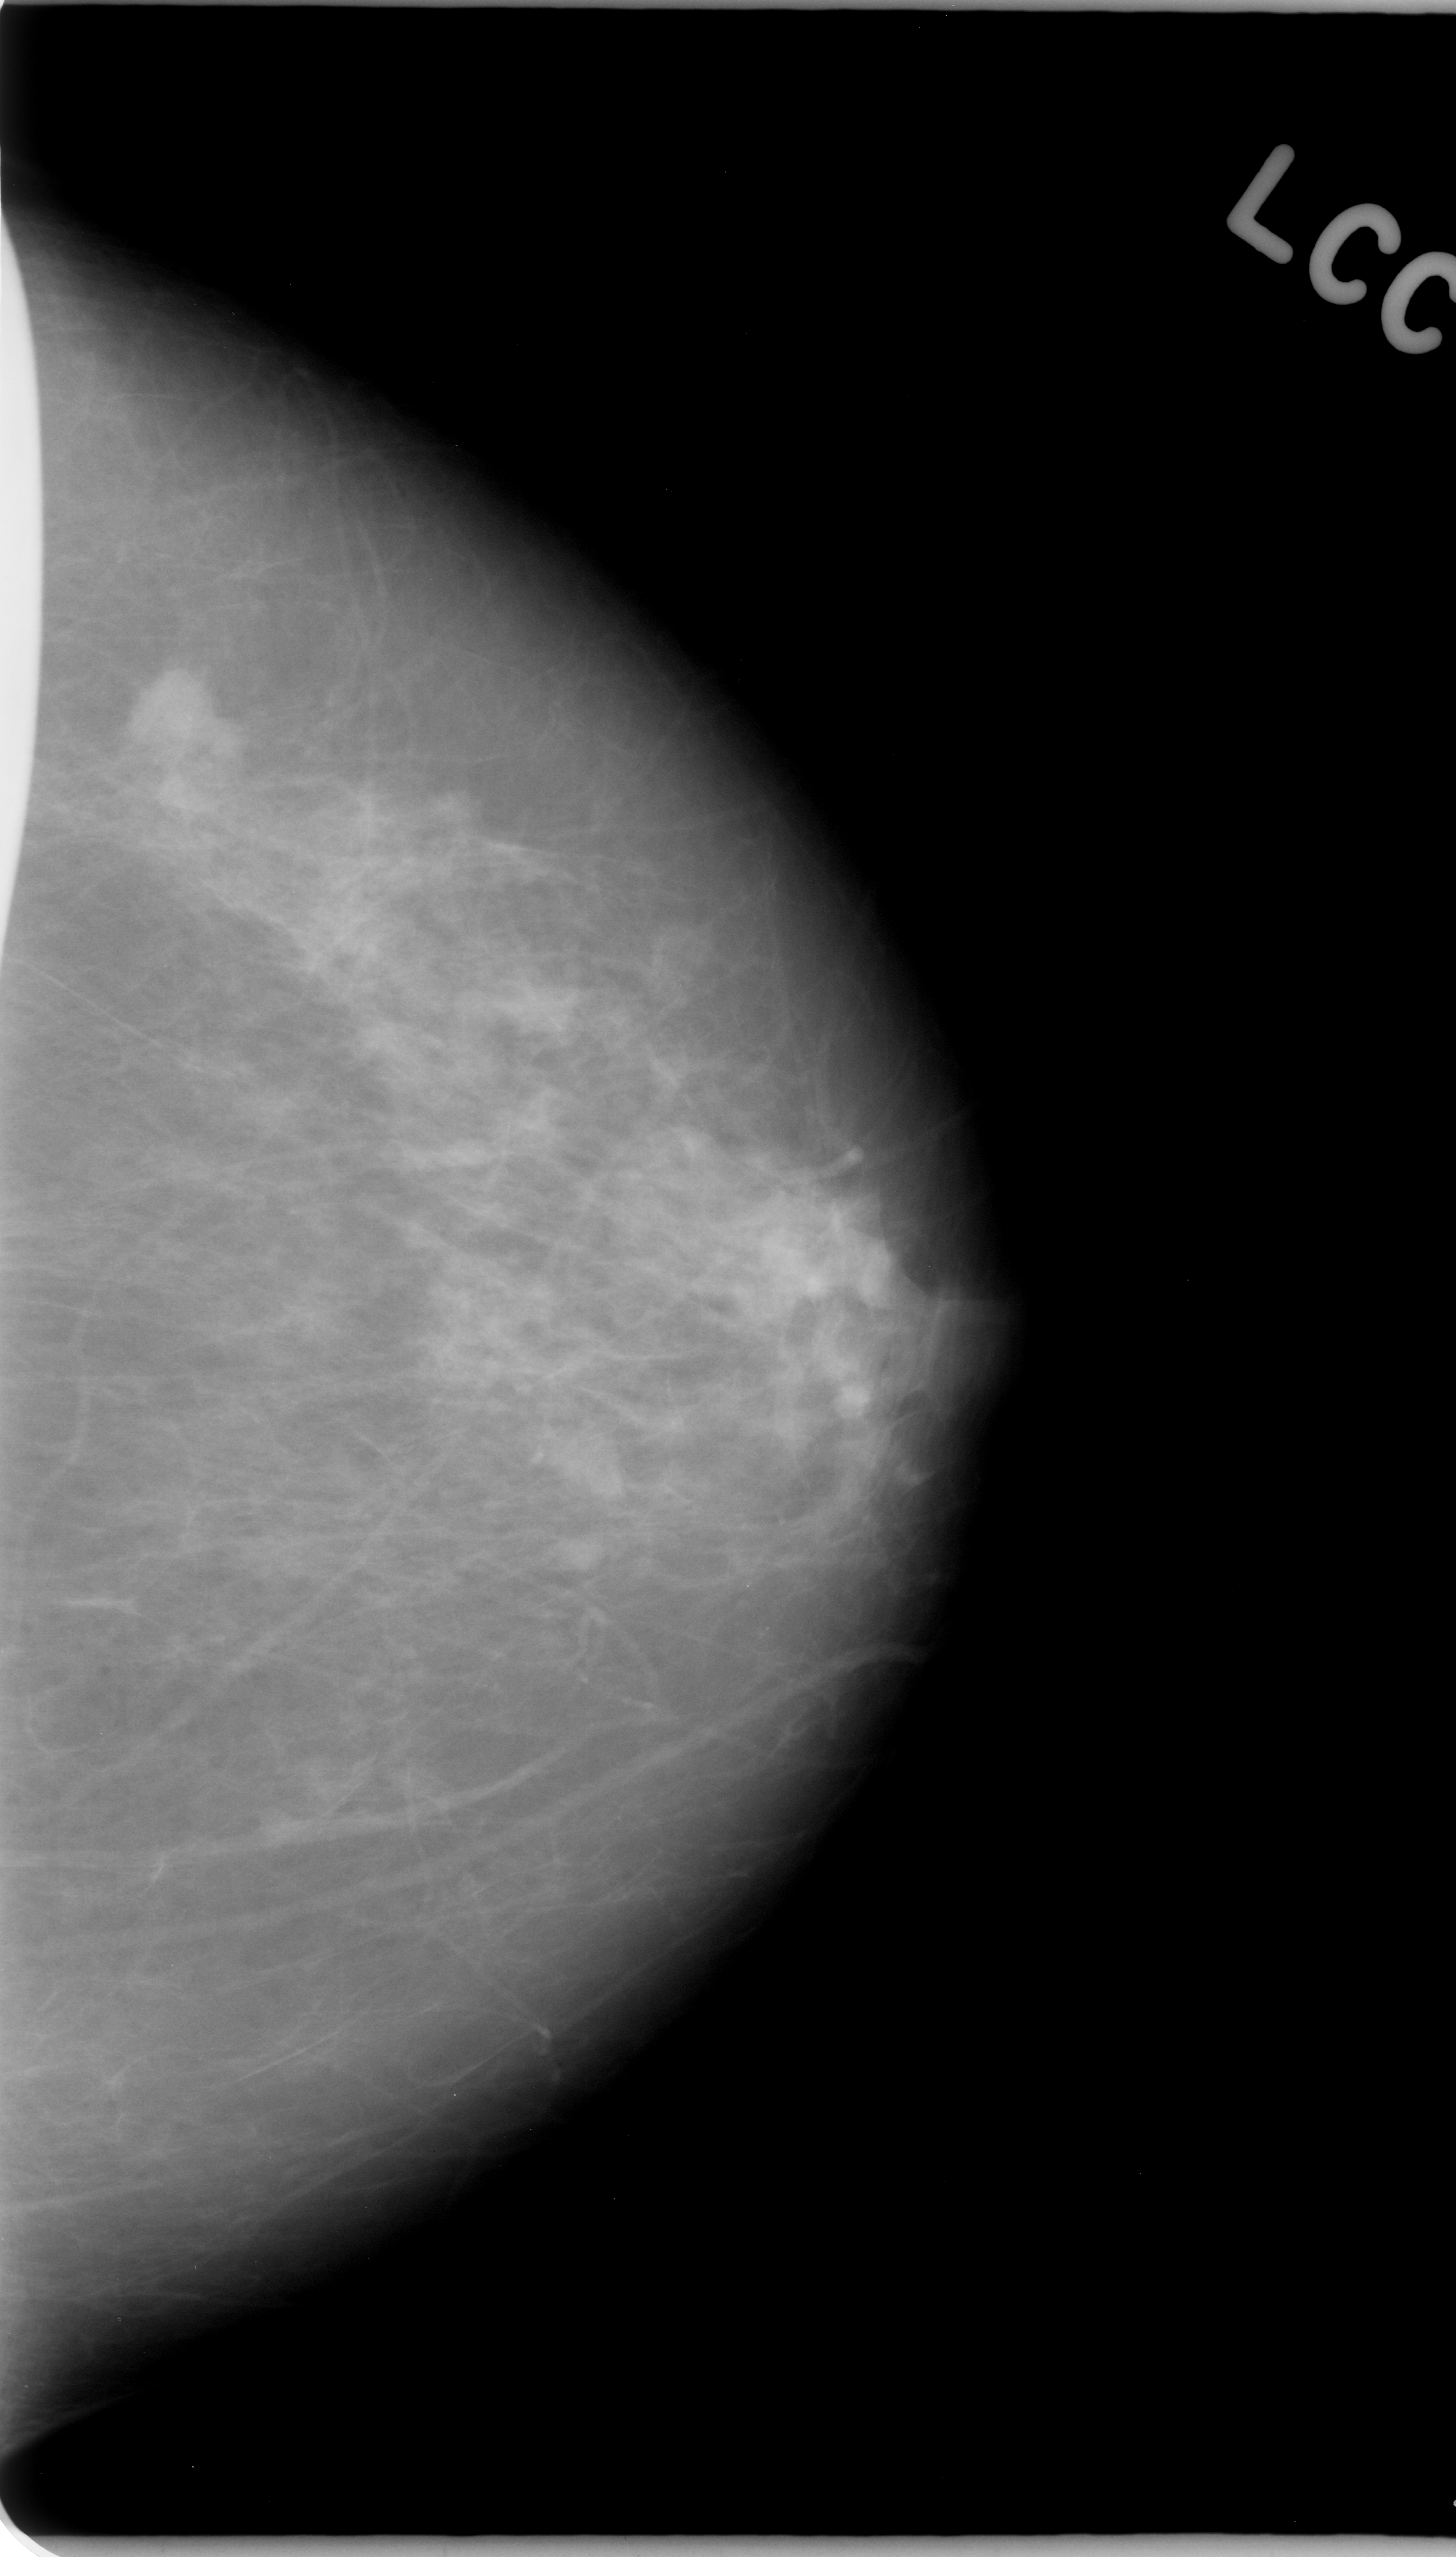
Digitized screen-film mammogram; left breast; CC view; 1456 × 2557 image matrix.
Expert-marked regions of interest on this film, with their recorded descriptors:
- mass, shape lobulated, margins microlobulated; BI-RADS assessment category 5; subtlety rating 5 on a 1 (subtle) to 5 (obvious) scale; pathology result (as recorded, not read from the image): malignant: bounding box (x1, y1, x2, y2) in pixels: (92, 654, 255, 830)